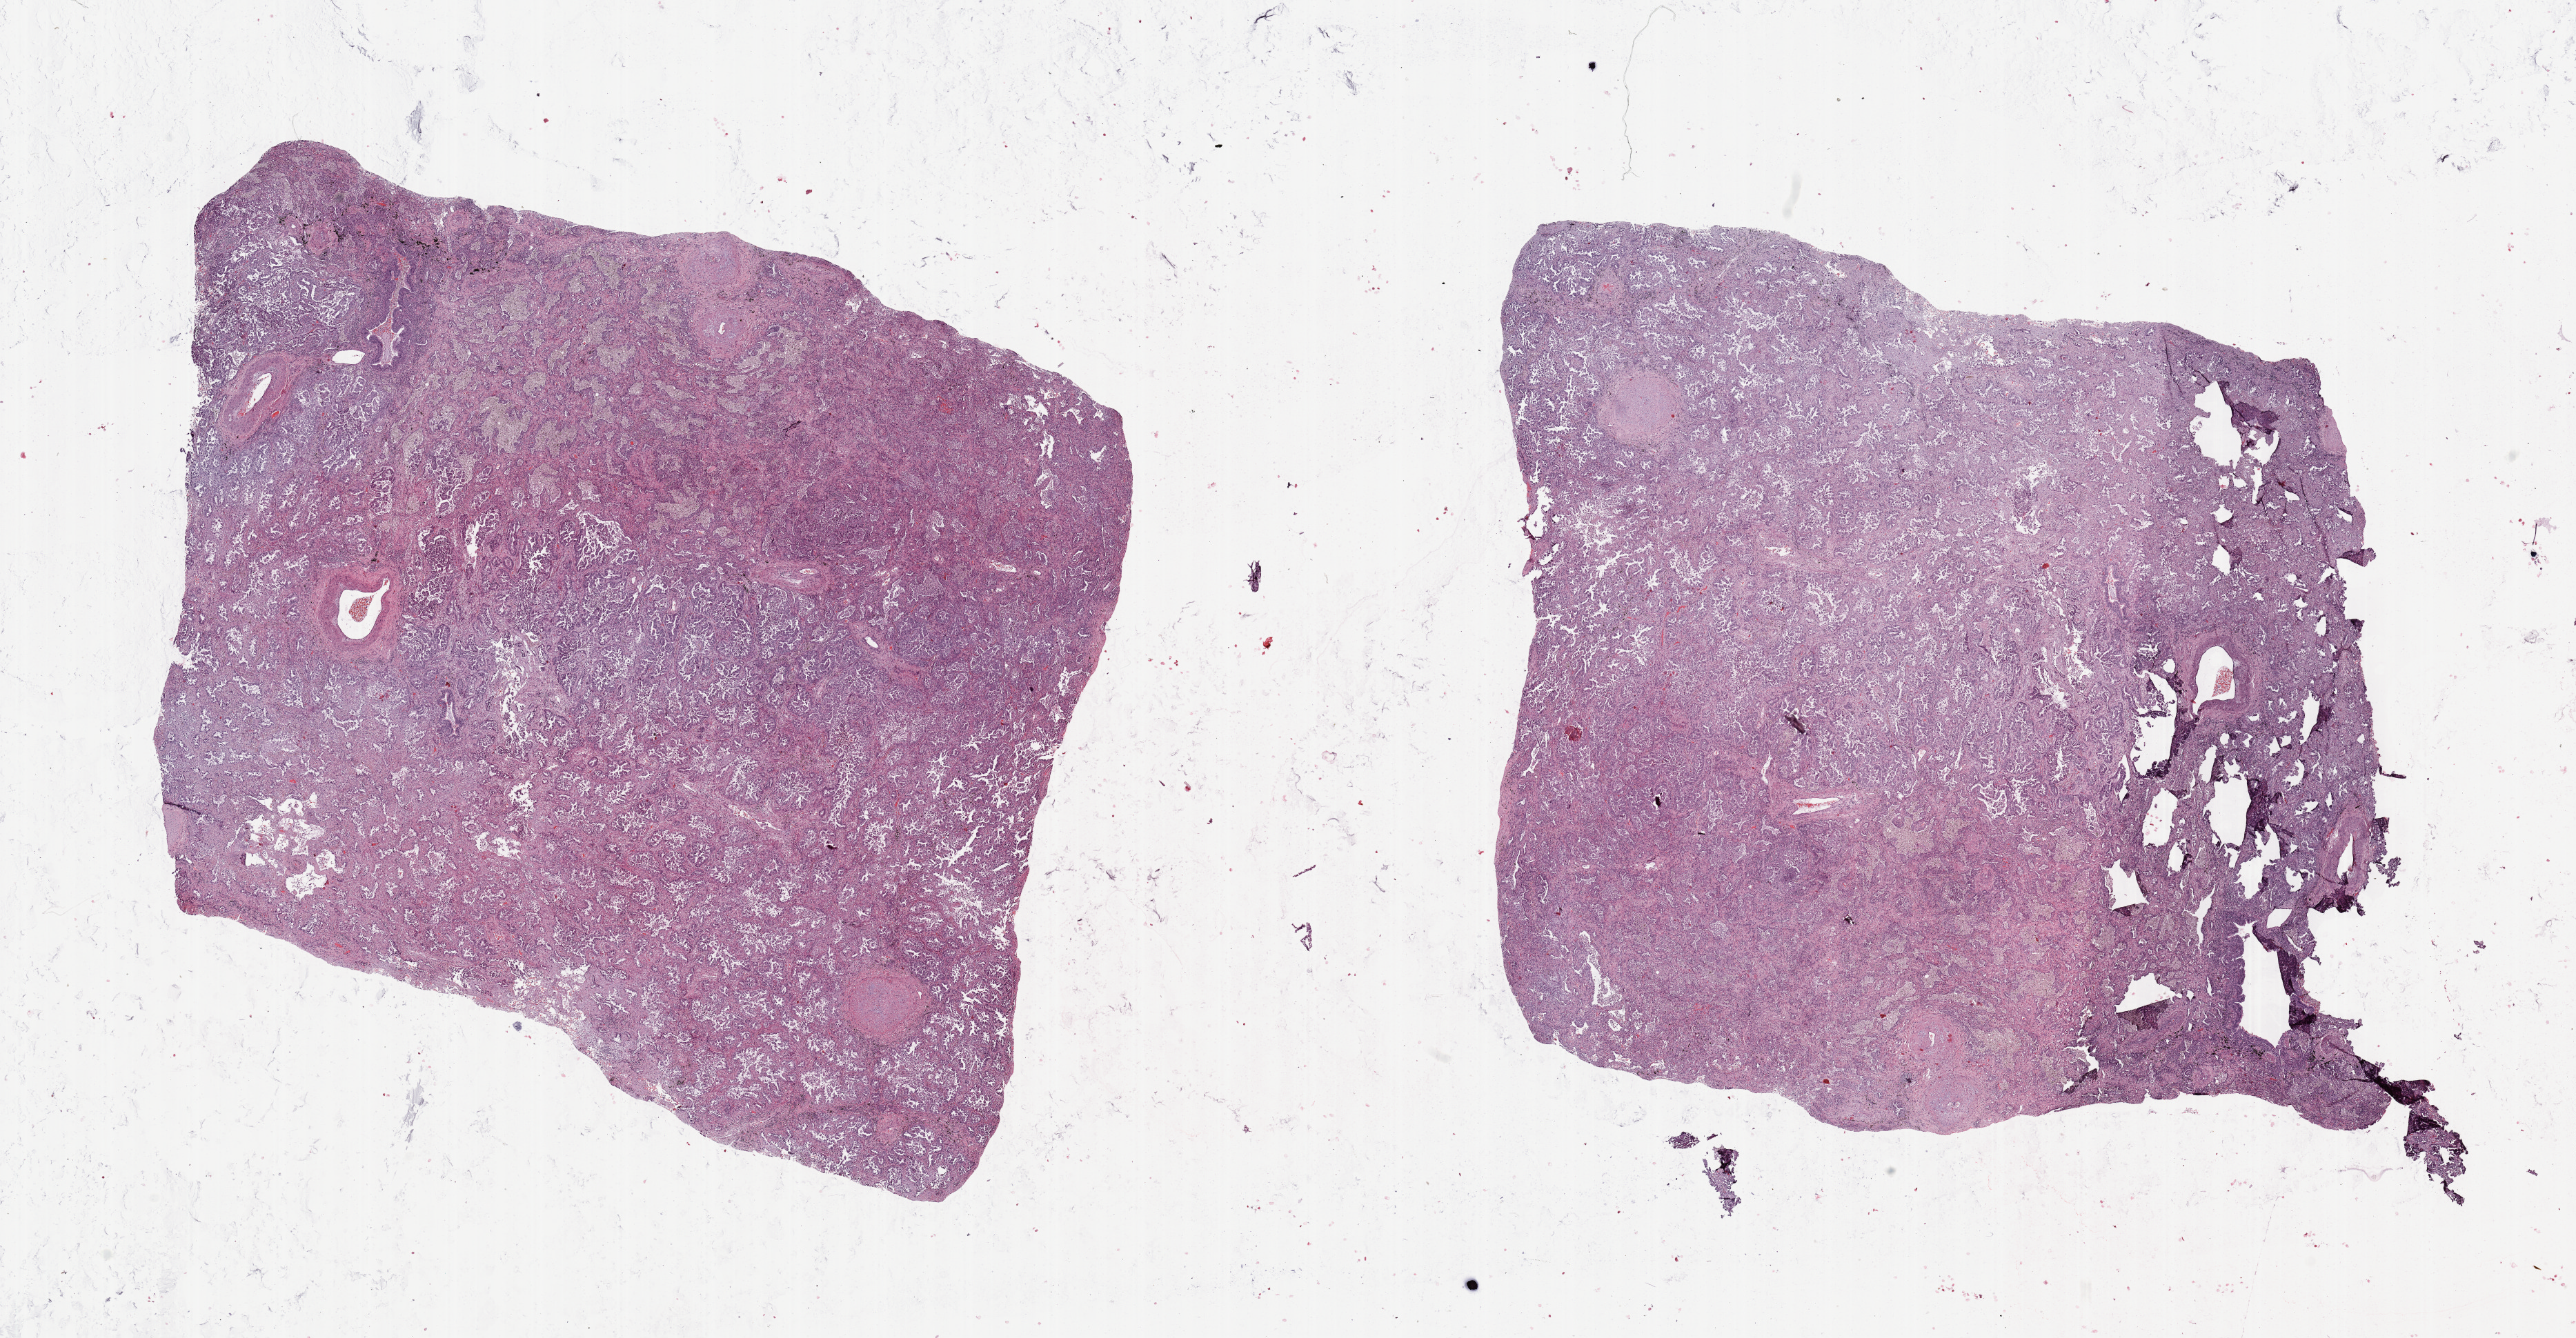
Digitized Hematoxylin and eosin (H&E) stained tissue section (whole slide), a low-resolution overview of the entire scanned area, about 29.5 x 15.3 mm, tumour tissue sample, sampled site: lung. Patient: male, age 59 years. Pathologist review of this section (percent, as recorded): tumour nuclei 75%, necrosis 5%.
Histologic diagnosis: Adenocarcinoma, NOS.